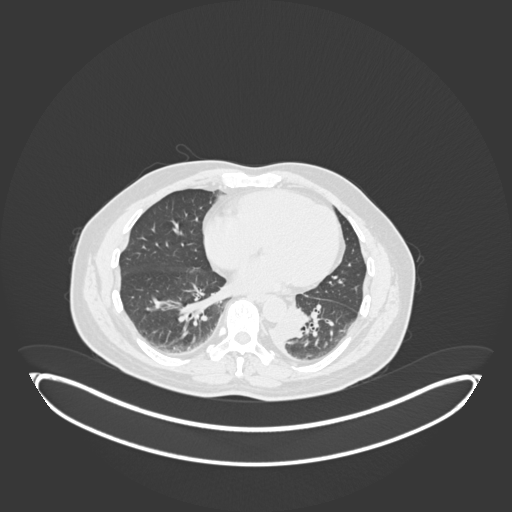
Chest CT, one axial slice; position 67 of 258 along the scan axis; 120 kVp; lung window (W 1500 / L -600 HU); 1 mm slice thickness; 512 × 512 image matrix. Patient: male, 54 years. From the clinical record (not read from this slice): clinical TNM (as recorded): T3 N0 M0.
Annotated regions visible in this slice (bounding box drawn by a radiologist):
- lung tumour (recorded histology: squamous cell carcinoma): bounding box (x1, y1, x2, y2) in pixels: (269, 314, 306, 347)